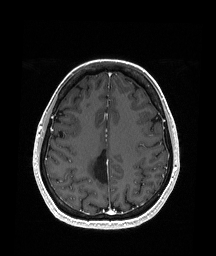
Brain MRI from a brain-tumour surgery series, one axial slice; position 67 of 151 along the scan axis; T1-weighted post-contrast; 216 × 256 image matrix, field of view 211 × 250 mm. From the clinical record (not read from this slice): histopathology: Oligodendroglioma; WHO grade: 2; IDH mutation: yes; tumour location: Right Parietal.
Annotated regions visible in this slice (outlined manually by an expert reader):
- previous resection cavity: bounding box (x1, y1, x2, y2) in pixels: (94, 149, 109, 183)